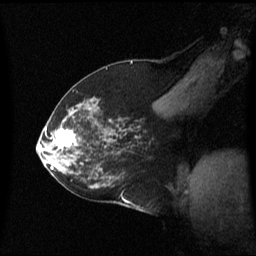
Breast MRI (dynamic contrast-enhanced), one sagittal slice; dynamic contrast-enhanced series, image 2 of 3 at this slice position (ordered by acquisition); 1.5 T; TE 4.2 ms, TR 8.4 ms; 256 × 256 image matrix, field of view 240 × 240 mm. Female patient, age 59 years. From the clinical record (not read from this slice): setting: breast cancer imaged before/during neoadjuvant chemotherapy; receptor status: HR-positive, HER2-negative.
Outlined on this slice (semi-automatically segmented with operator editing):
- analysis volume of interest (the breast-tissue region the enhancement analysis was run in; not a lesion): box from (x=46, y=114) to (x=89, y=163) px
- tumour enhancement mask (voxels above the 70 % enhancement threshold inside the analysis volume of interest): (x=53, y=130)–(x=75, y=149)